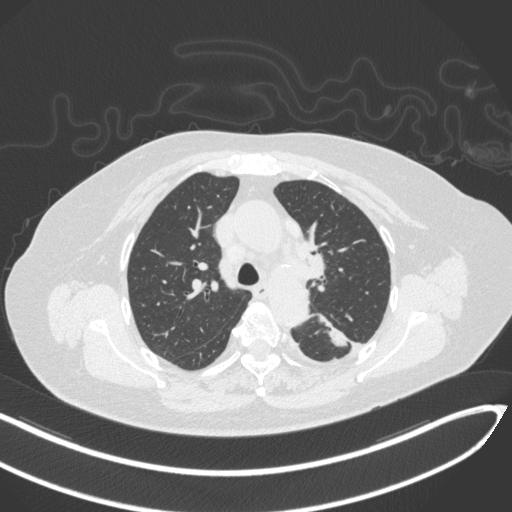
Chest CT, one axial slice; position 219 of 270 along the scan axis; reconstruction kernel B31f; lung window (W 1500 / L -600 HU); 1 mm slice thickness; 512 × 512 image matrix, field of view 400 × 400 mm. Patient: female, 76 years. From the clinical record (not read from this slice): clinical TNM (as recorded): T1c N0 M0.
Outlined on this slice (bounding box drawn by a radiologist):
- lung tumour (recorded histology: adenocarcinoma): bounding box (x1, y1, x2, y2) in pixels: (317, 302, 355, 351)